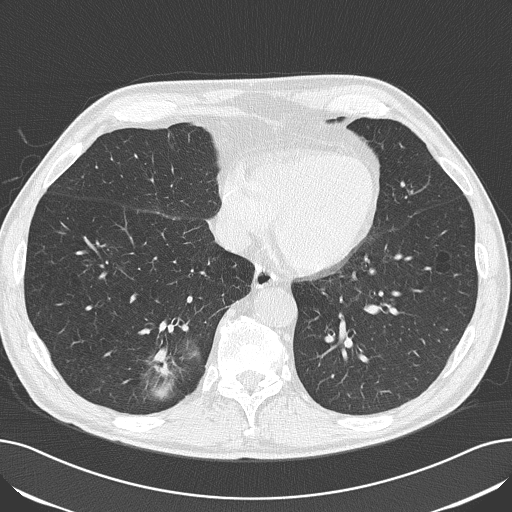
Low-dose screening chest CT, one axial slice. Position 58 of 182 along the scan axis. Reconstruction kernel B50f. 120 kVp. Lung window (W 1500 / L -600 HU). 2 mm slice thickness. 512 × 512 image matrix, field of view 368 × 368 mm.
Outlined on this slice (expert manual segmentation):
- lesion 1 (tumor, lower lobe of right lung): bounding box <154,362,175,388> (left, top, right, bottom; pixels)